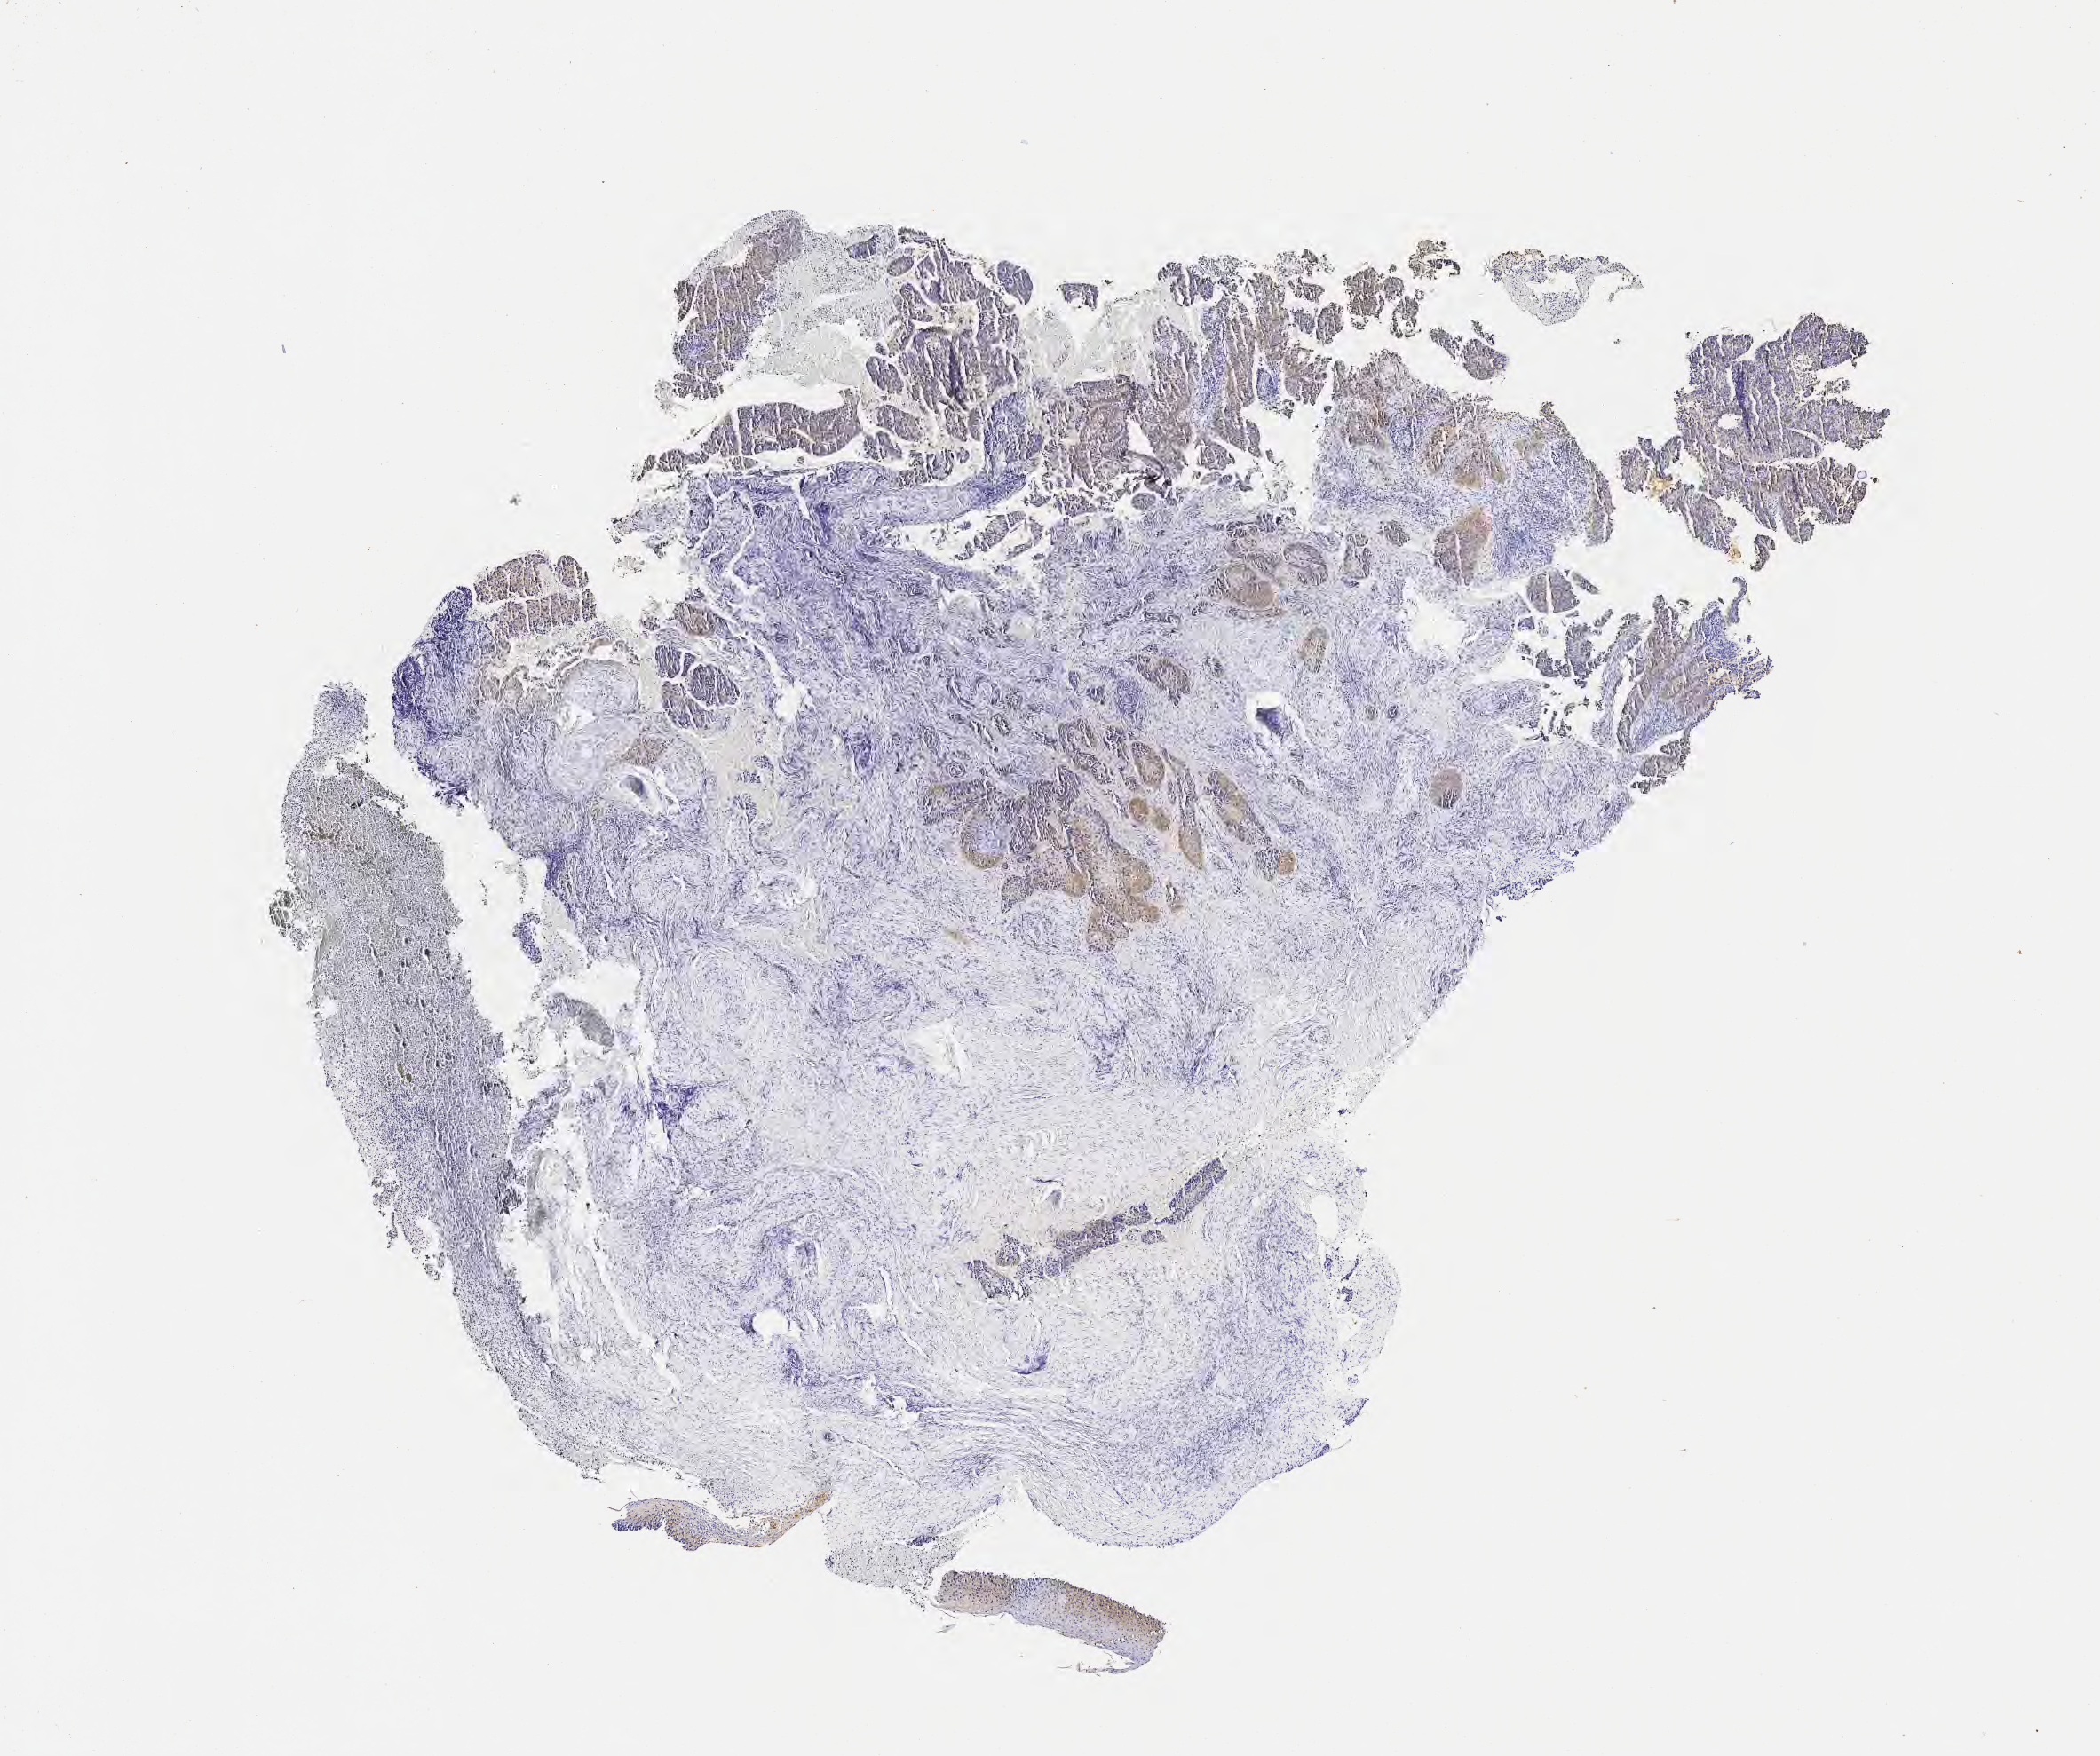
Immunohistochemistry (IHC) whole-slide image stained for p16 (p16INK4a), low-resolution overview of the scanned area, about 9.6 x 8.0 mm, tumor tissue, anatomic site: cervix. Female patient, age 45 years.
Diagnosis: Squamous cell carcinoma, large cell, nonkeratinizing, NOS.